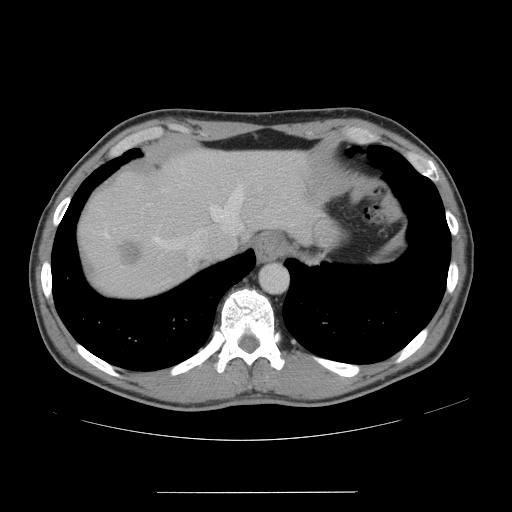
Contrast-enhanced abdominal CT, one axial slice; position 130 of 178 along the scan axis; 120 kVp; intravenous contrast given; soft-tissue window (W 400 / L 40 HU); 512 × 512 image matrix. Male patient, age 53 years. Case-level facts recorded for this patient, not image findings: diagnosis: colorectal cancer liver metastases, imaged before liver resection; multiple liver metastases: yes; largest metastasis: 2.4 cm; chemotherapy before resection: yes.
Structures marked on this image (expert manual segmentation):
- hepatic veins: bounding box [x1, y1, x2, y2] px = [104, 185, 244, 256]
- liver: [79, 152, 311, 297]
- planned liver remnant (the part of the liver to remain after resection): [170, 151, 310, 237]
- liver metastasis: [117, 237, 146, 266]